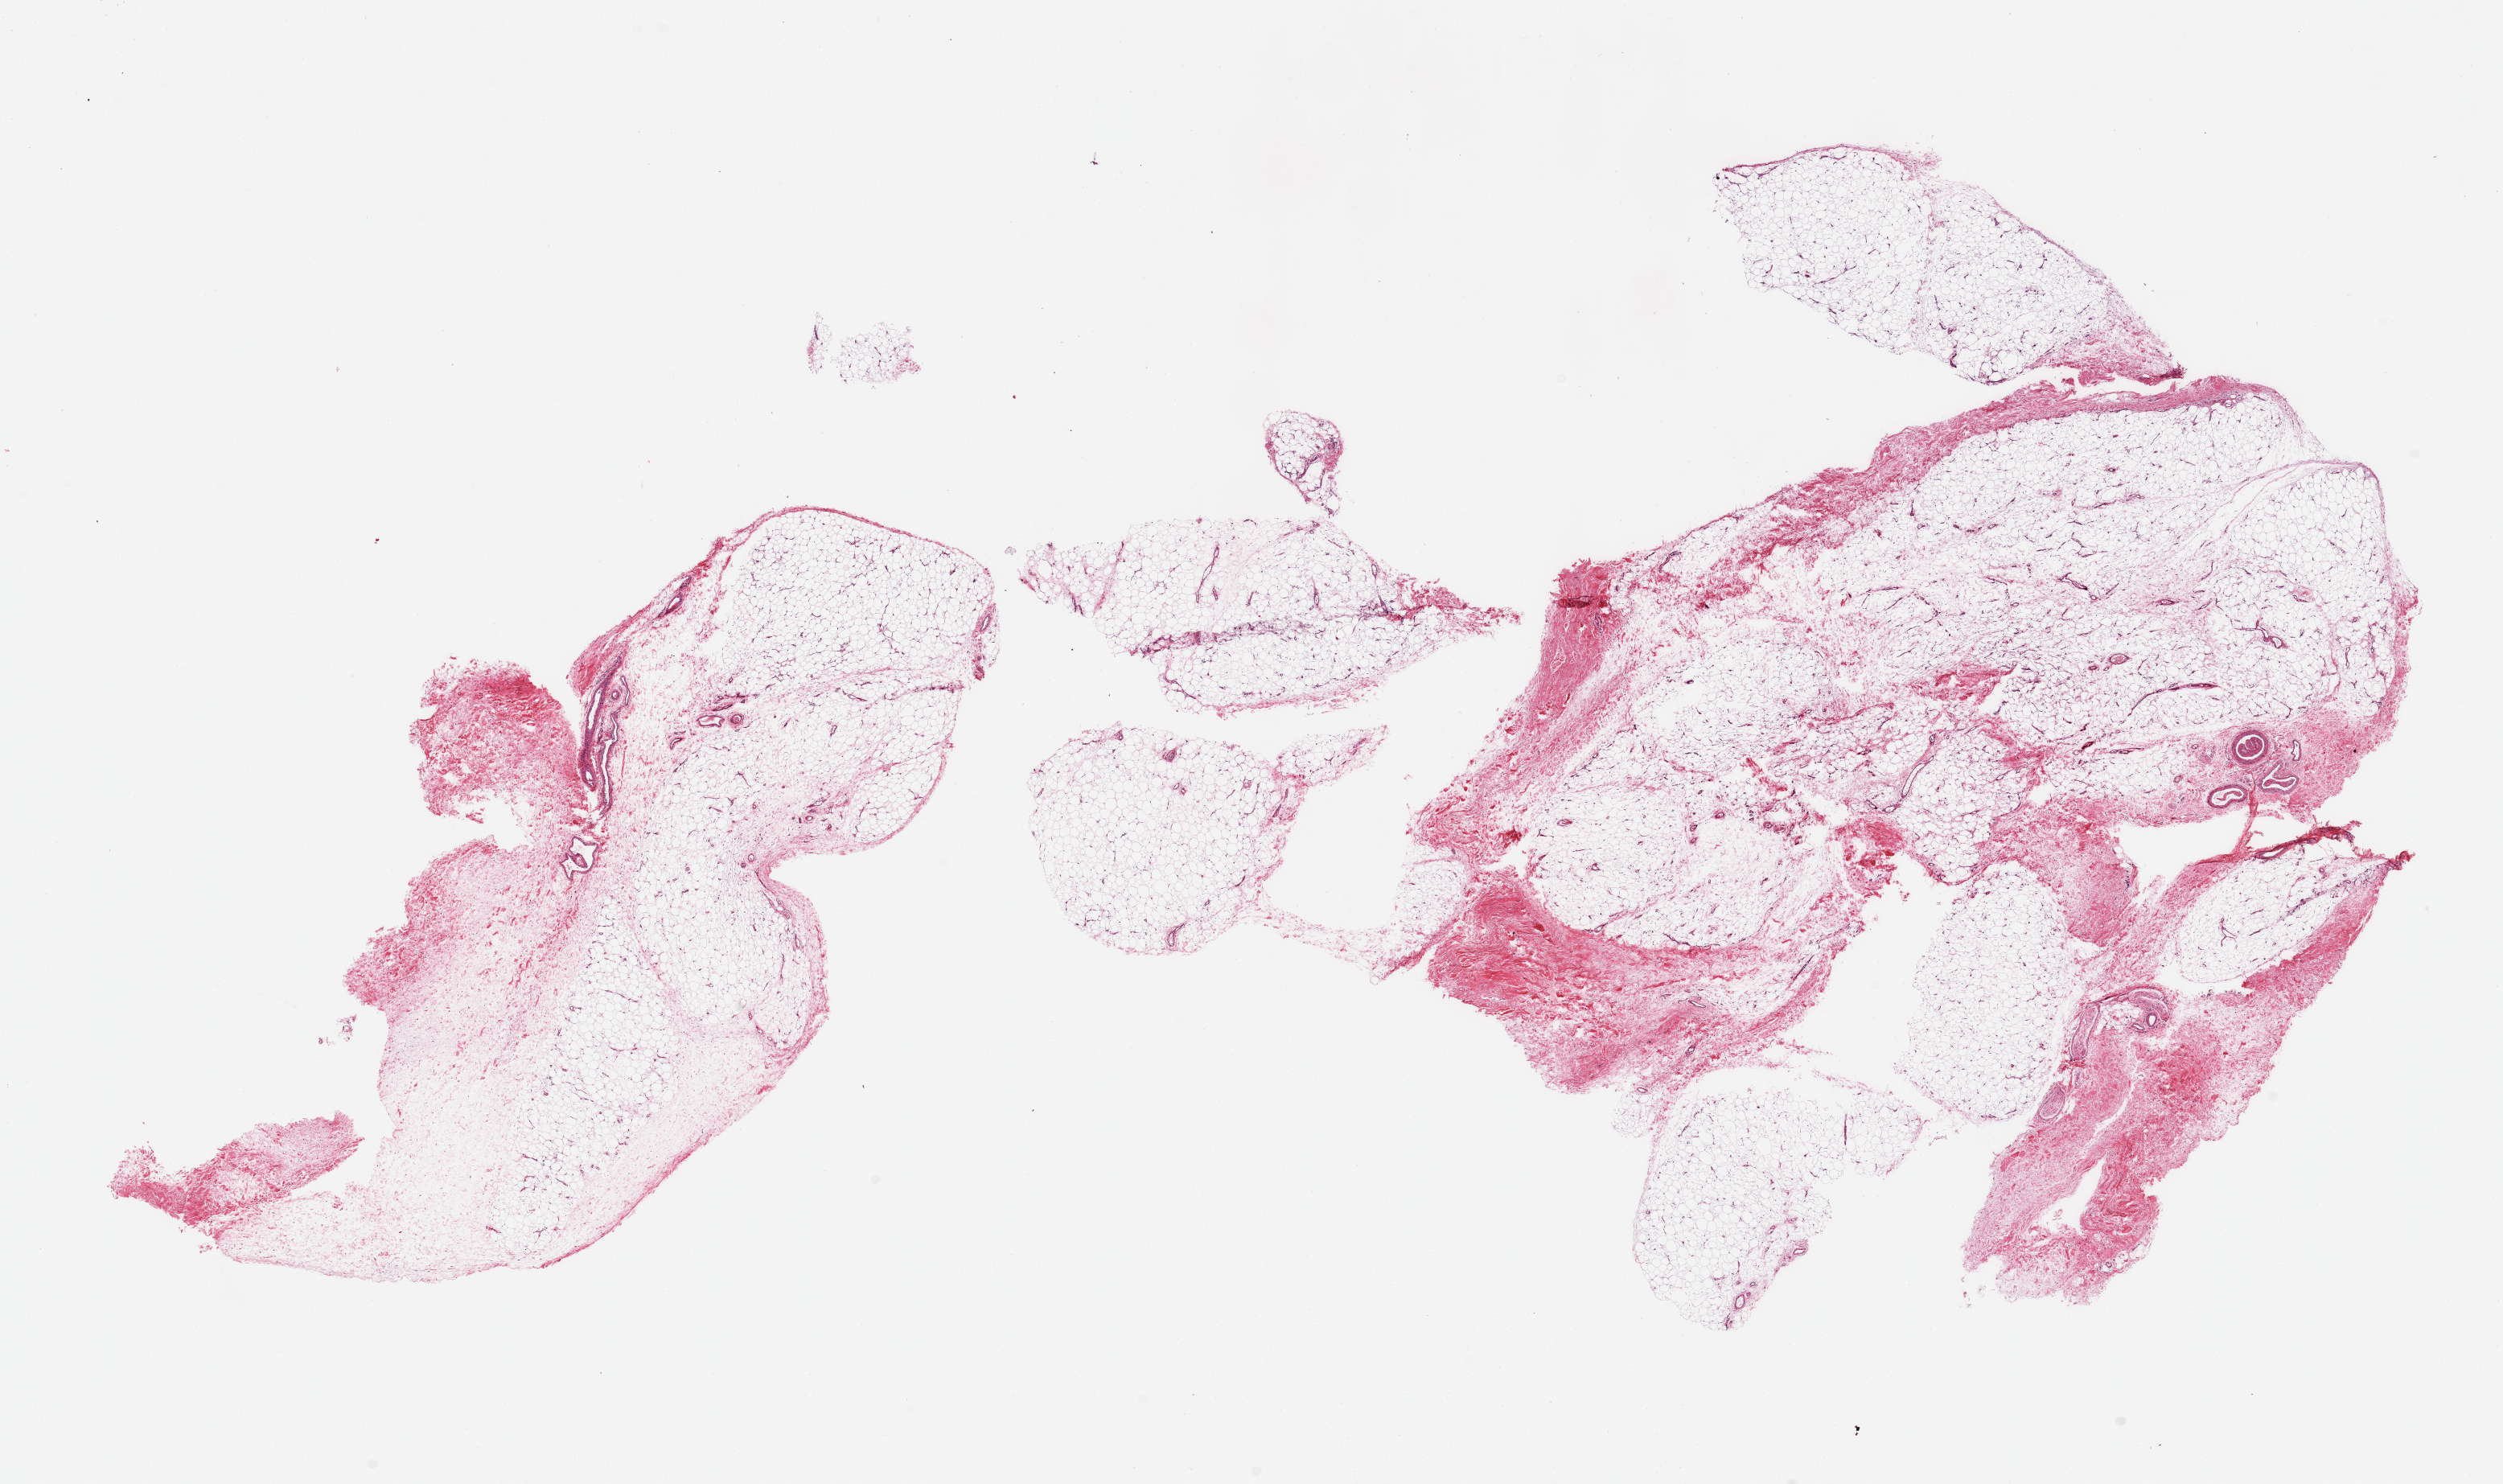
Hematoxylin and eosin (H&E) whole-slide image, whole scanned area (about 24.6 x 14.6 mm) shown as a low-resolution overview. PAXgene-fixed paraffin-embedded (PFPE) section. Sampled site (target tissue): adipose tissue. Donor tissue sample. Donor: male.
Reviewer comment on this tissue sample: 2 pieces, ~20% fascia.